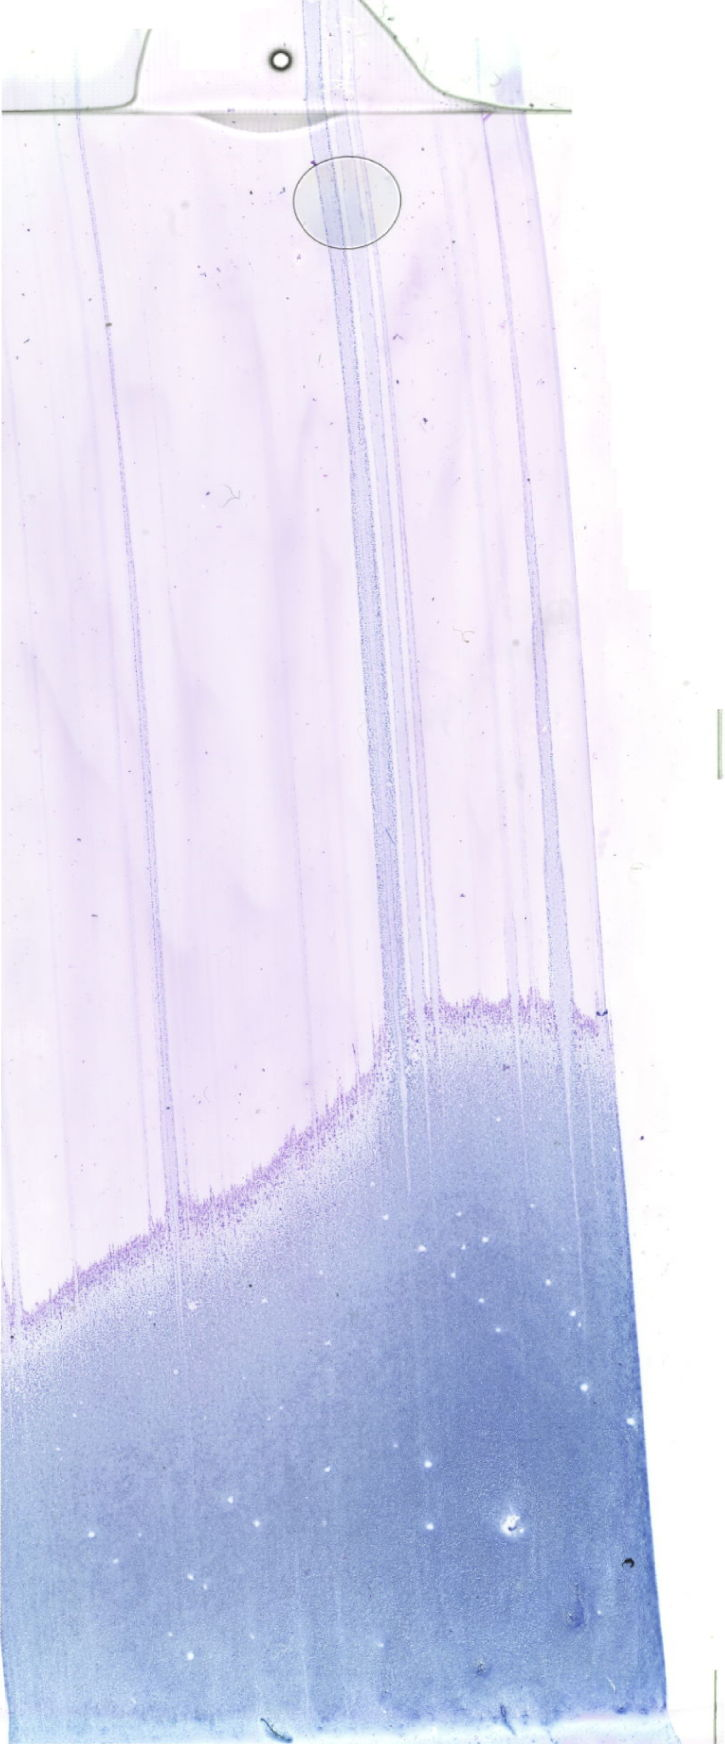
May-Grünwald–Giemsa-stained marrow aspirate smear (whole slide), low-resolution overview of the scanned area, about 20.6 x 49.4 mm. Female patient.
Diagnosis: Acute Myeloid Leukemia with Maturation.